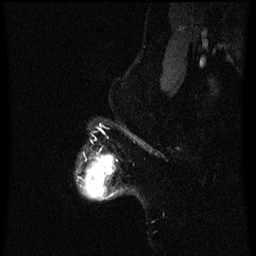
Breast MRI (dynamic contrast-enhanced), one sagittal slice. Position 57 of 60 along the scan axis. Dynamic contrast-enhanced series, image 2 of 3 at this slice position (ordered by acquisition). 1.5 T. TE 4.2 ms, TR 8 ms. 2 mm slice thickness. 256 × 256 image matrix, field of view 190 × 190 mm. Patient: female, 50 years.
Annotated regions visible in this slice (semi-automatically segmented with operator editing):
- analysis volume of interest (the breast-tissue region the enhancement analysis was run in; not a lesion): bounding box (x1, y1, x2, y2) in pixels: (76, 153, 118, 201)
- tumour enhancement mask (voxels above the 70 % enhancement threshold inside the analysis volume of interest): (82, 155, 115, 199)